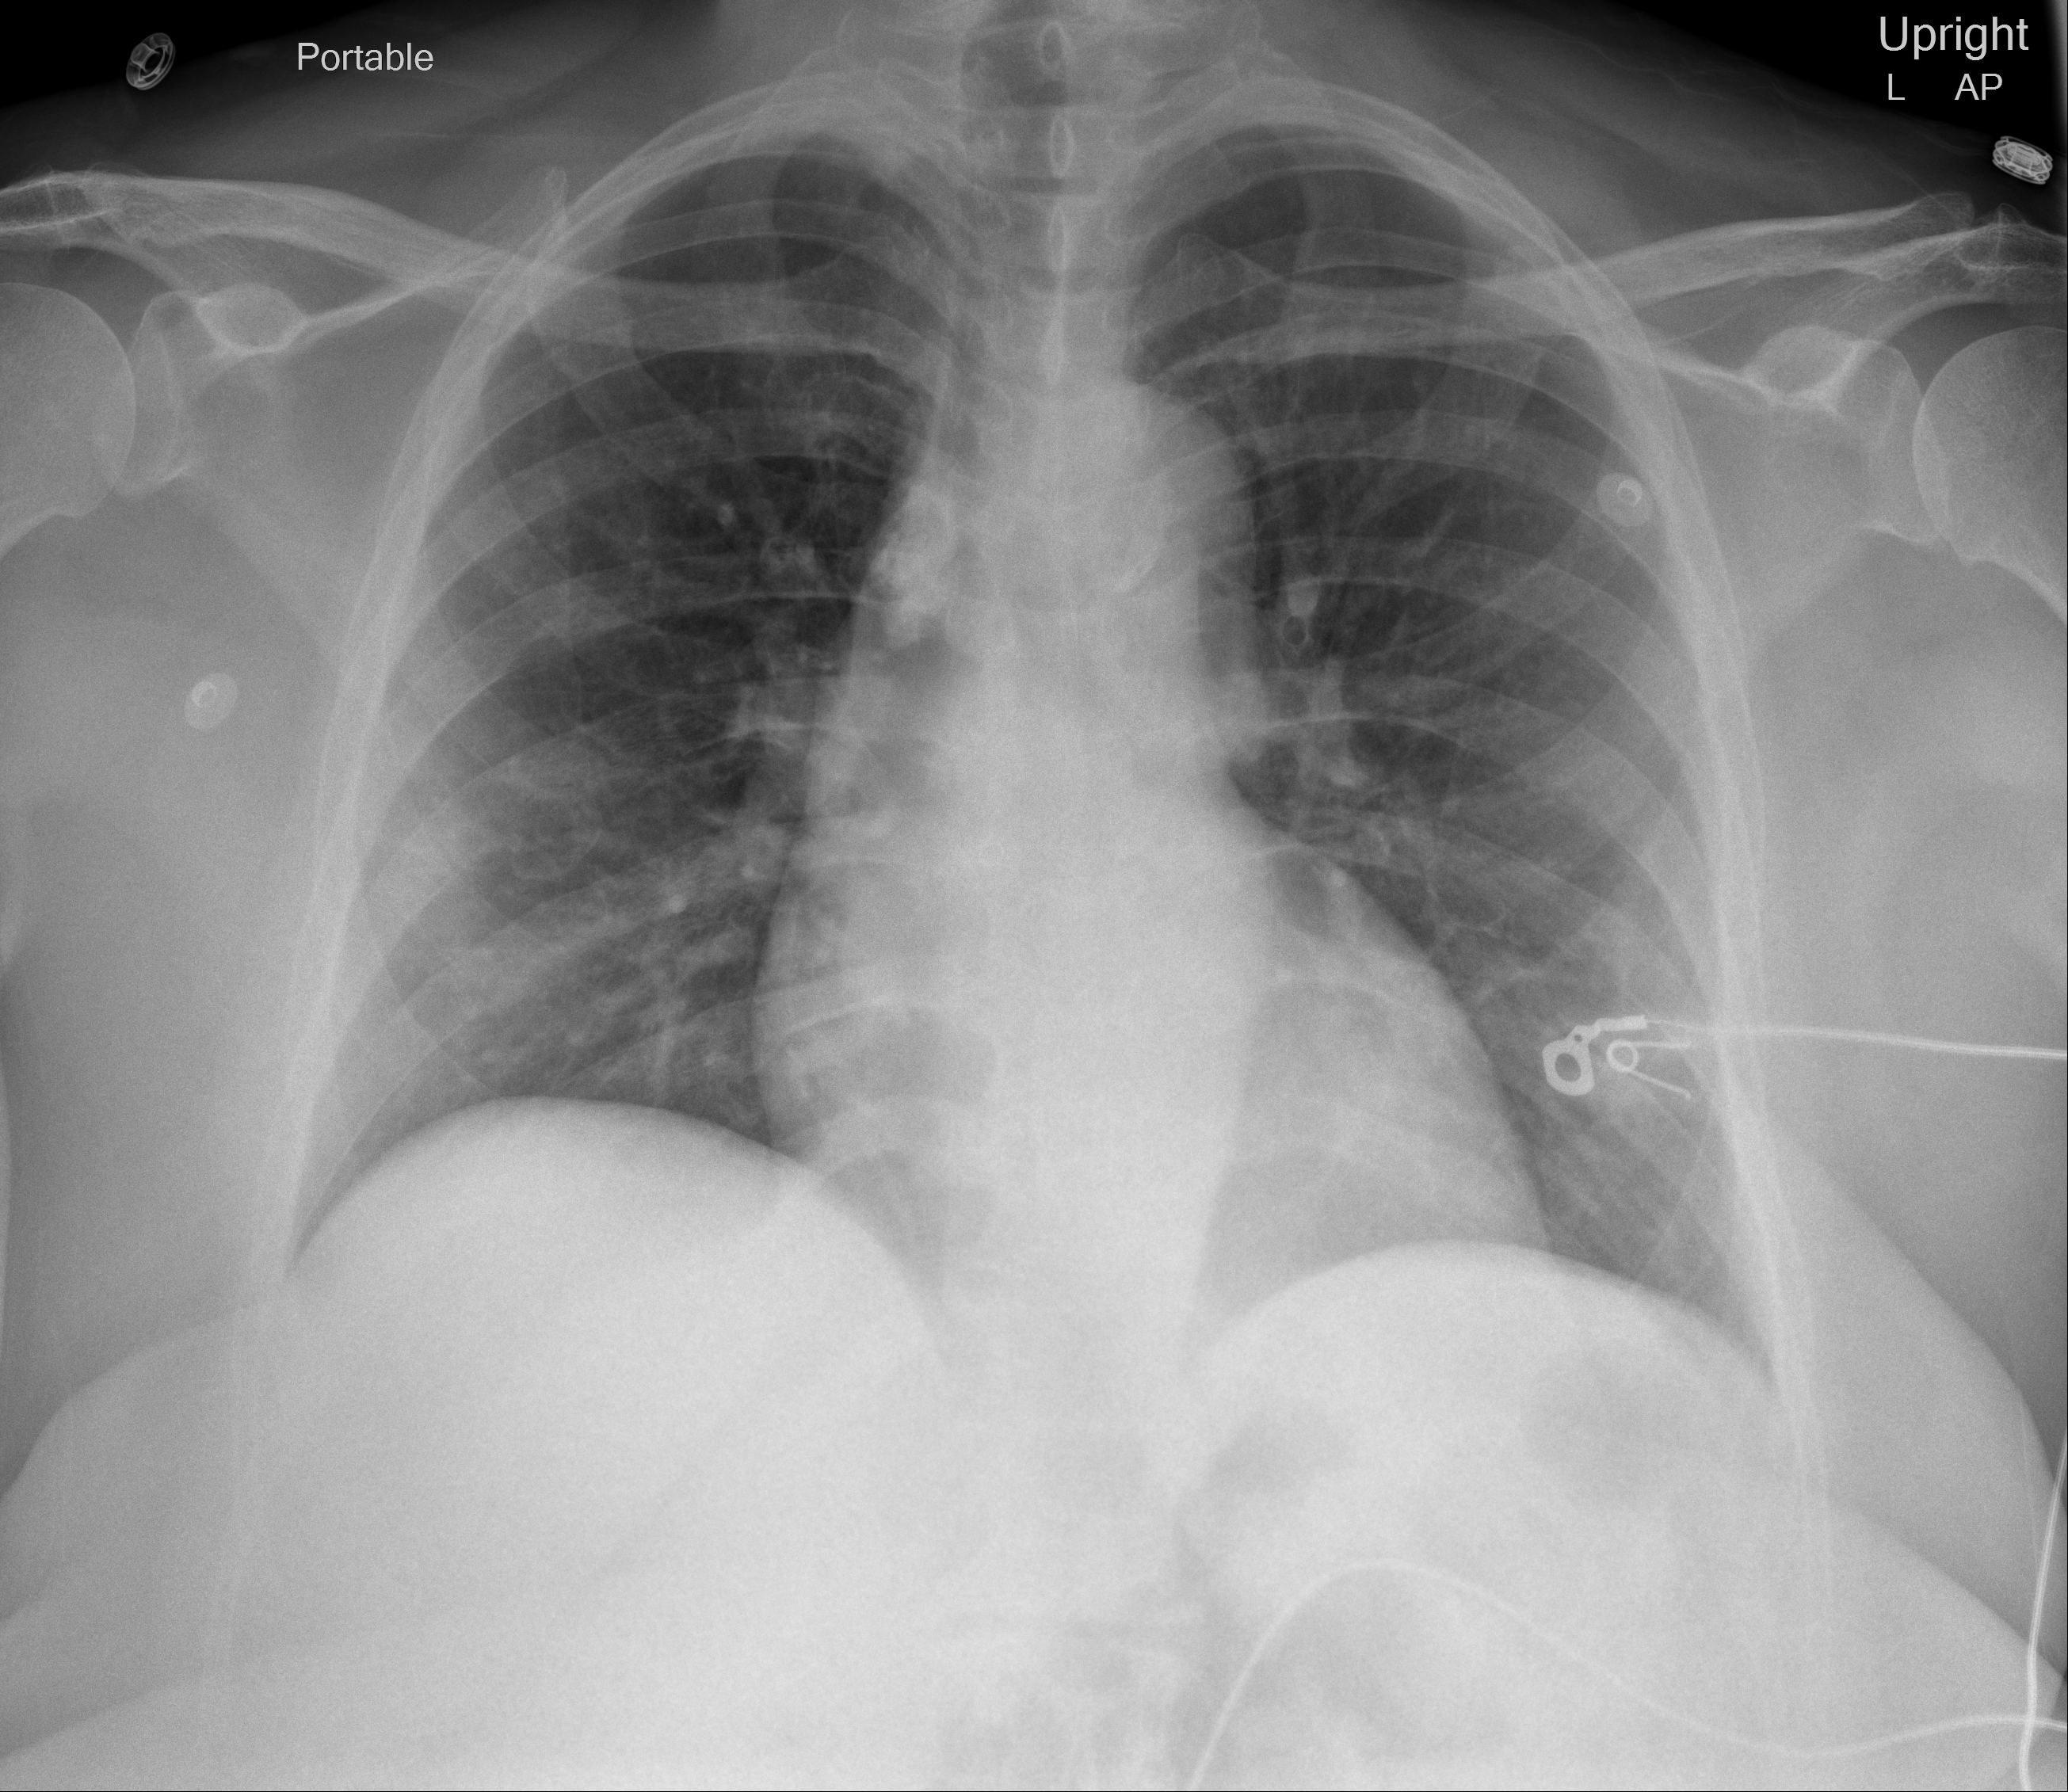
Portable chest radiograph, AP projection. Female patient, age 59 years; COVID-19 (test-positive).
Key findings recorded by the radiologist: lungs are clear and without focal consolidation.